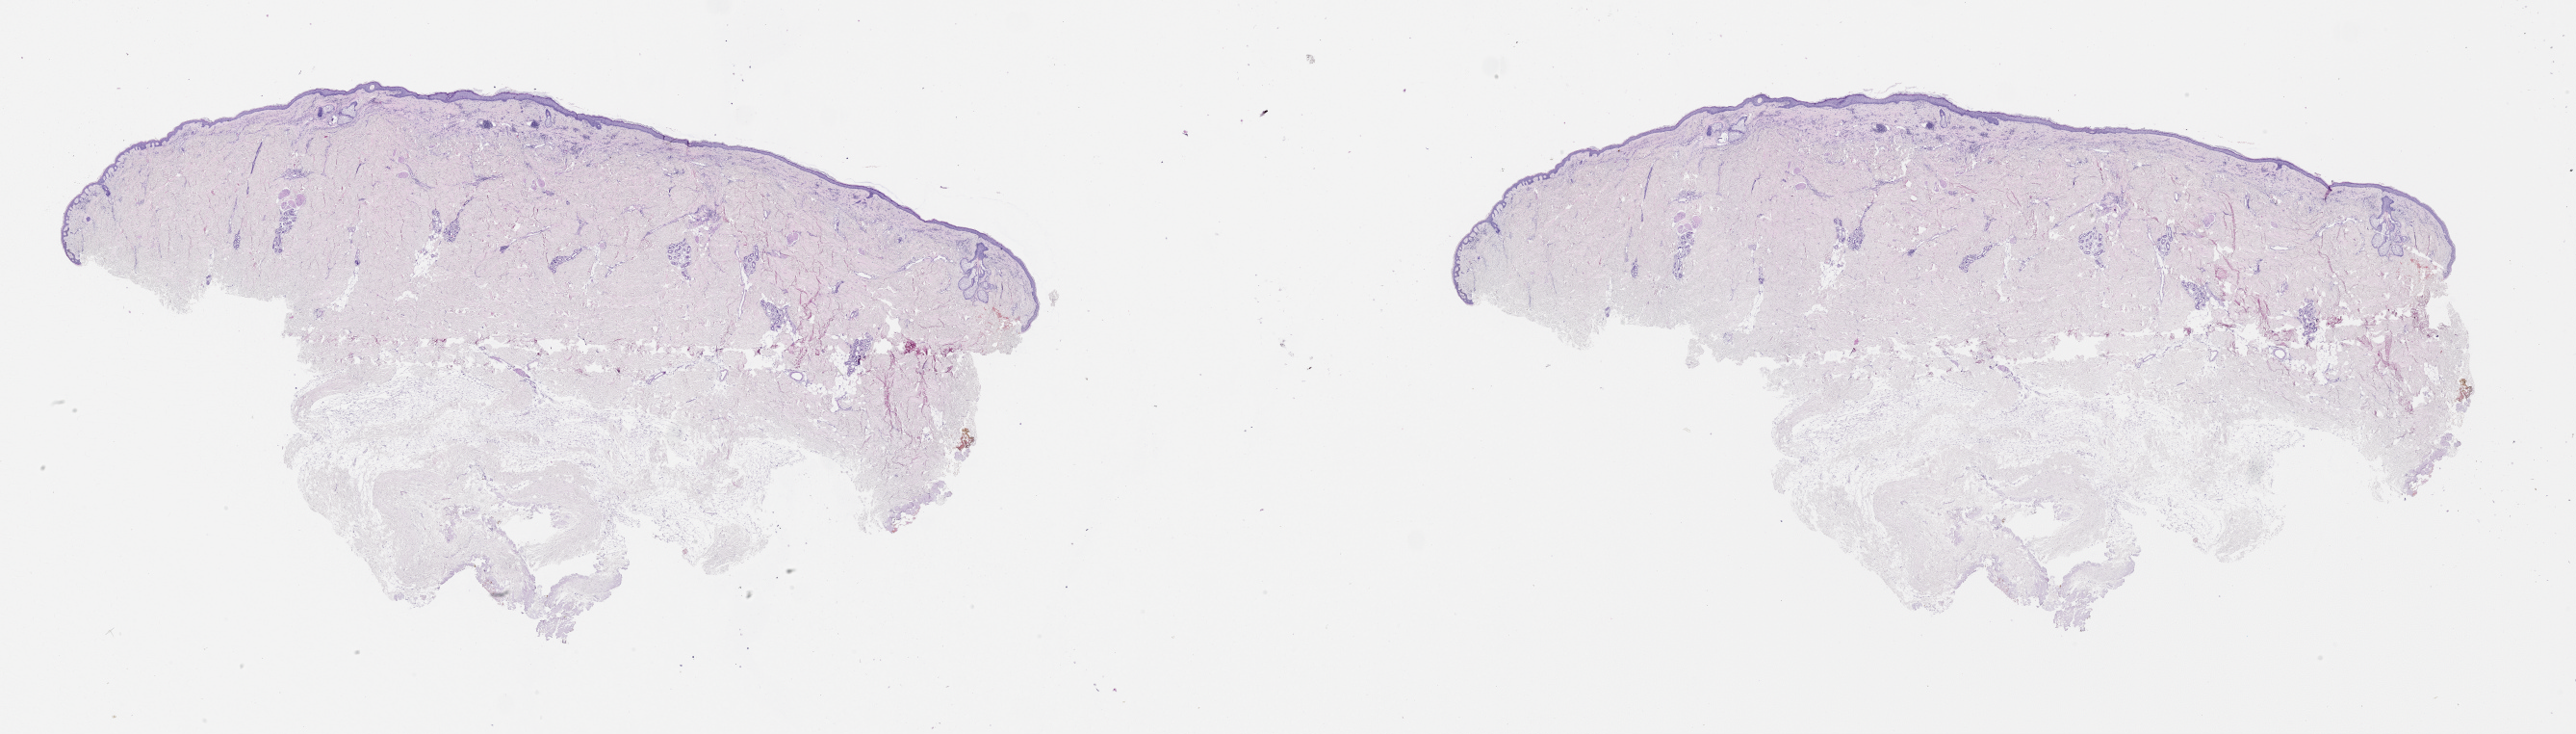
Whole-slide histology image, H&E-stained — a low-resolution overview of the entire scanned area, about 43.1 x 12.3 mm (slide scanned at 20x); normal (non-tumour) tissue sample, sampled site: trunk. Male, 82 y/o.
This section: normal (non-tumour) tissue from the same patient. Patient diagnosis: Malignant melanoma, NOS.